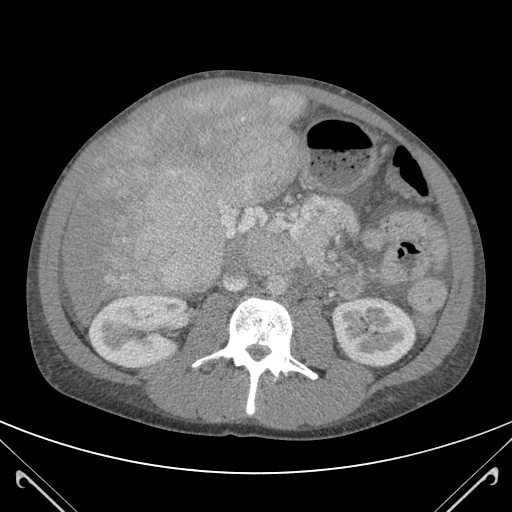
Contrast-enhanced abdominal CT (liver protocol), one axial slice; slice 50 of 118 in the series (ordered by position); soft-tissue window (W 400 / L 40 HU); 3 mm slice thickness; 512 × 512 image matrix. From the clinical record (not read from this slice): diagnosis: hepatocellular carcinoma (patient treated with transarterial chemoembolisation; whether this scan precedes or follows treatment is not stated here); TNM stage (as recorded): Stage-IIIB.
Outlined on this slice (semi-automatically segmented with operator editing):
- abdominal aorta: bounding box [x1, y1, x2, y2] px = [266, 276, 286, 296]
- liver parenchyma outside the tumour (the mass and vessels are separate outlines, so this box may not span the whole liver): [60, 84, 307, 318]
- mass: [91, 86, 304, 298]
- liver vessels: [106, 277, 115, 281]